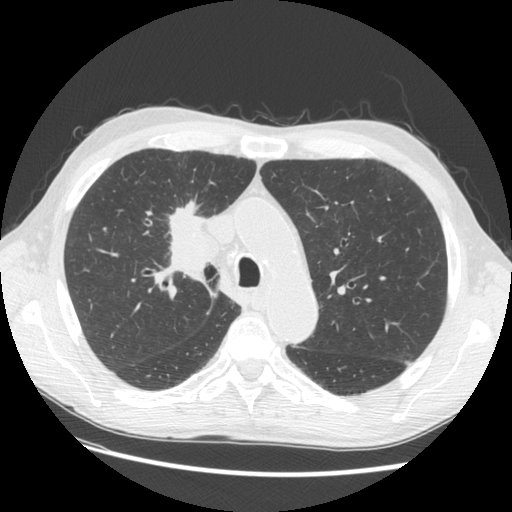
Low-dose screening chest CT, axial slice. Third annual screen. Lung window (W 1500 / L -600 HU). Standard (soft-tissue) reconstruction kernel (STANDARD). 512 × 512 image matrix. Male participant, aged 73 years at enrolment. Current smoker at enrolment.
Expert reader's lesion annotation, bounding box [x1, y1, x2, y2] px = [142, 184, 234, 277]. The screening reader recorded 4 non-calcified nodules or masses ≥4 mm on this exam (right upper lobe, right upper lobe, right upper lobe, left lower lobe); which of them this box marks is not recorded. Later outcome: lung cancer diagnosed 48 days after this screen — squamous cell carcinoma, NOS, right upper lobe, poorly differentiated (G3), stage IIIB (AJCC 6th edition), 56 mm at pathology.